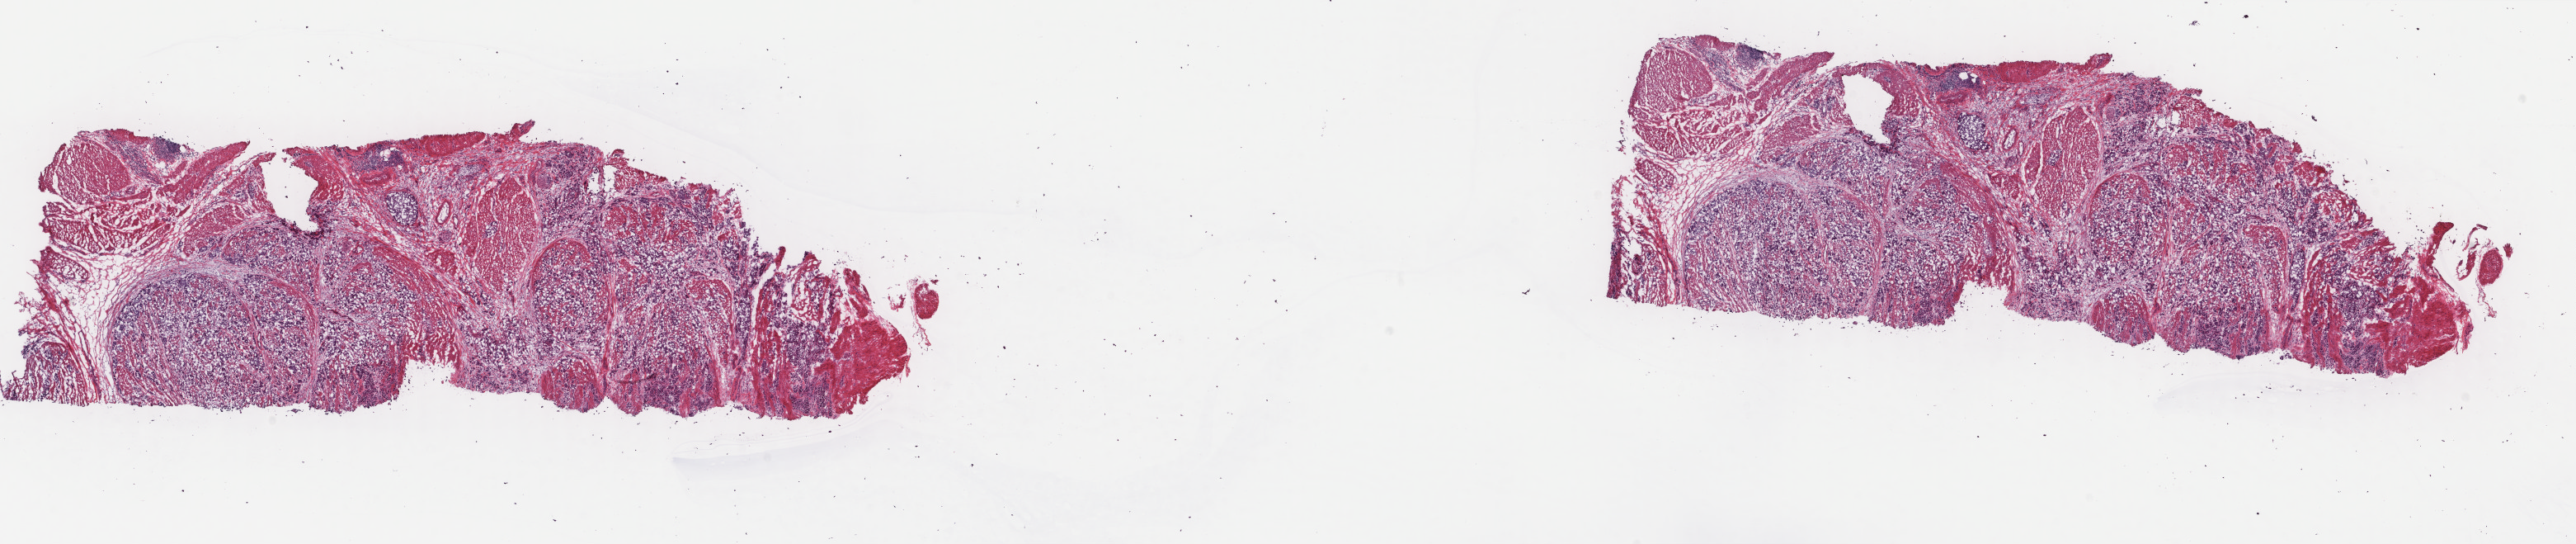
Digitized H&E-stained tissue section (whole slide), a low-resolution overview of the entire scanned area, about 24.8 x 5.2 mm (slide scanned at 40x), frozen section from the top of the tissue portion, bladder, primary tumour sample. Male, age 60 years at initial diagnosis. Histologic grade: high grade. Slide review estimates, as recorded: tumour cells 75%, tumour nuclei 75%, normal cells 0%, stromal cells 25%, necrosis 0%. Inflammatory infiltration, as recorded: lymphocyte infiltration 3%, monocyte infiltration 0%, neutrophil infiltration 0%.
AJCC pathologic stage: IV (7th edition). Diagnosis: Transitional cell carcinoma (posterior wall of bladder). TNM: T4a N2 M1.